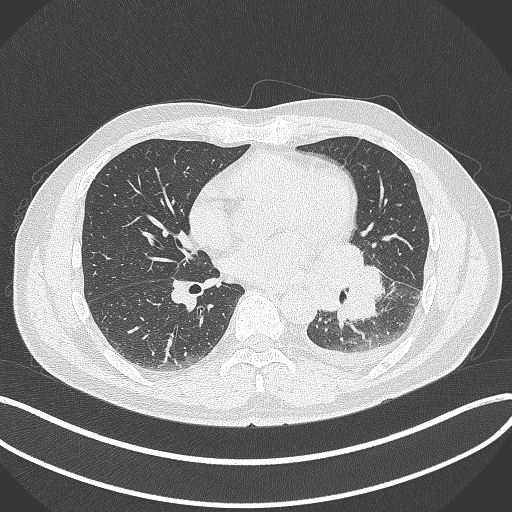
Chest CT, one axial slice. Reconstruction kernel B70f. Lung window (W 1500 / L -600 HU). 1 mm slice thickness. 512 × 512 image matrix, field of view 400 × 400 mm. Male patient, age 58 years. Case-level facts recorded for this patient, not image findings: clinical TNM (as recorded): T3 N1 M1b.
Annotated regions visible in this slice (bounding box drawn by a radiologist):
- lung tumour (recorded histology: small cell carcinoma): bounding box <314,245,381,329> (left, top, right, bottom; pixels)